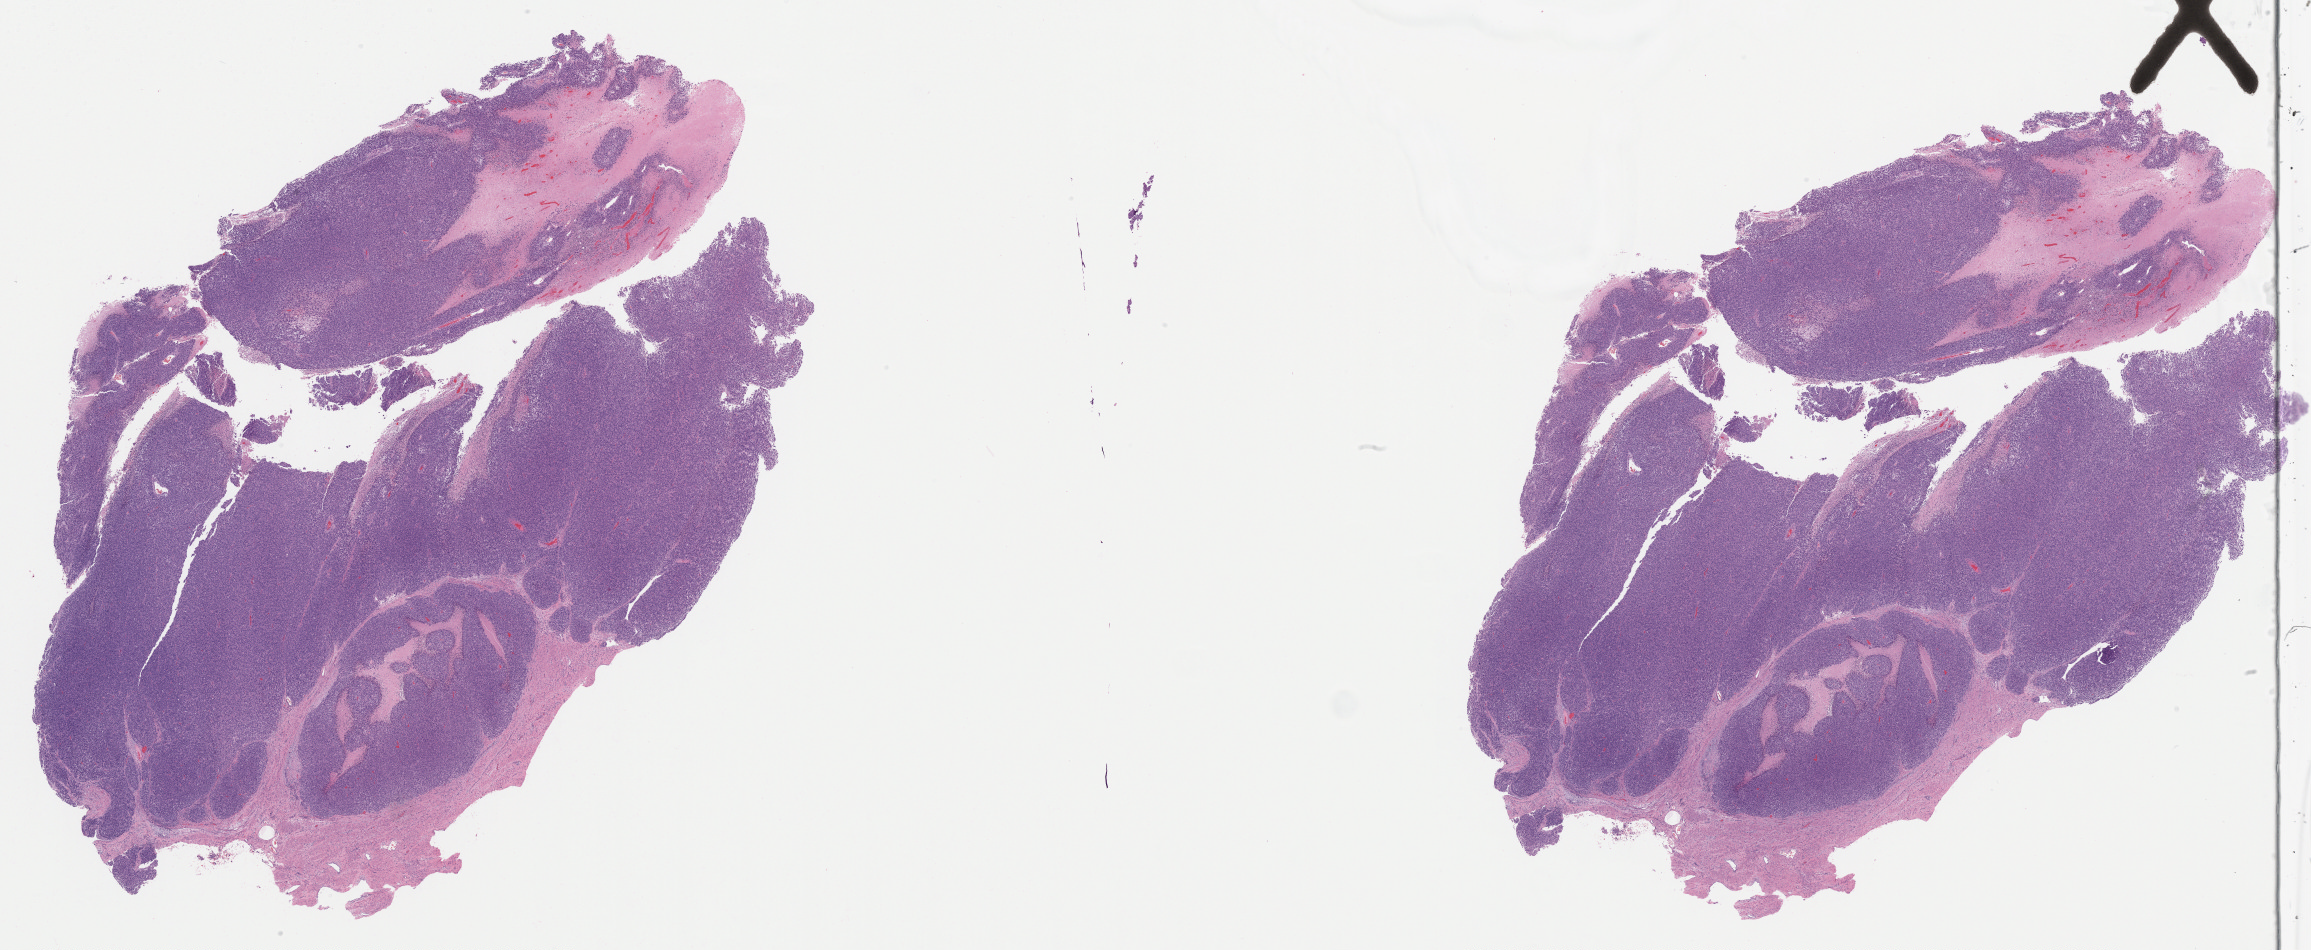
Hematoxylin and eosin (H&E) stained whole-slide image, whole scanned area (about 37.0 x 15.2 mm, from a 20x scan) shown as a low-resolution overview; formalin-fixed paraffin-embedded (FFPE) diagnostic section; primary tumour sample from the uterus. Female, age 58 years at initial diagnosis.
Pathologic diagnosis: Leiomyosarcoma, NOS.